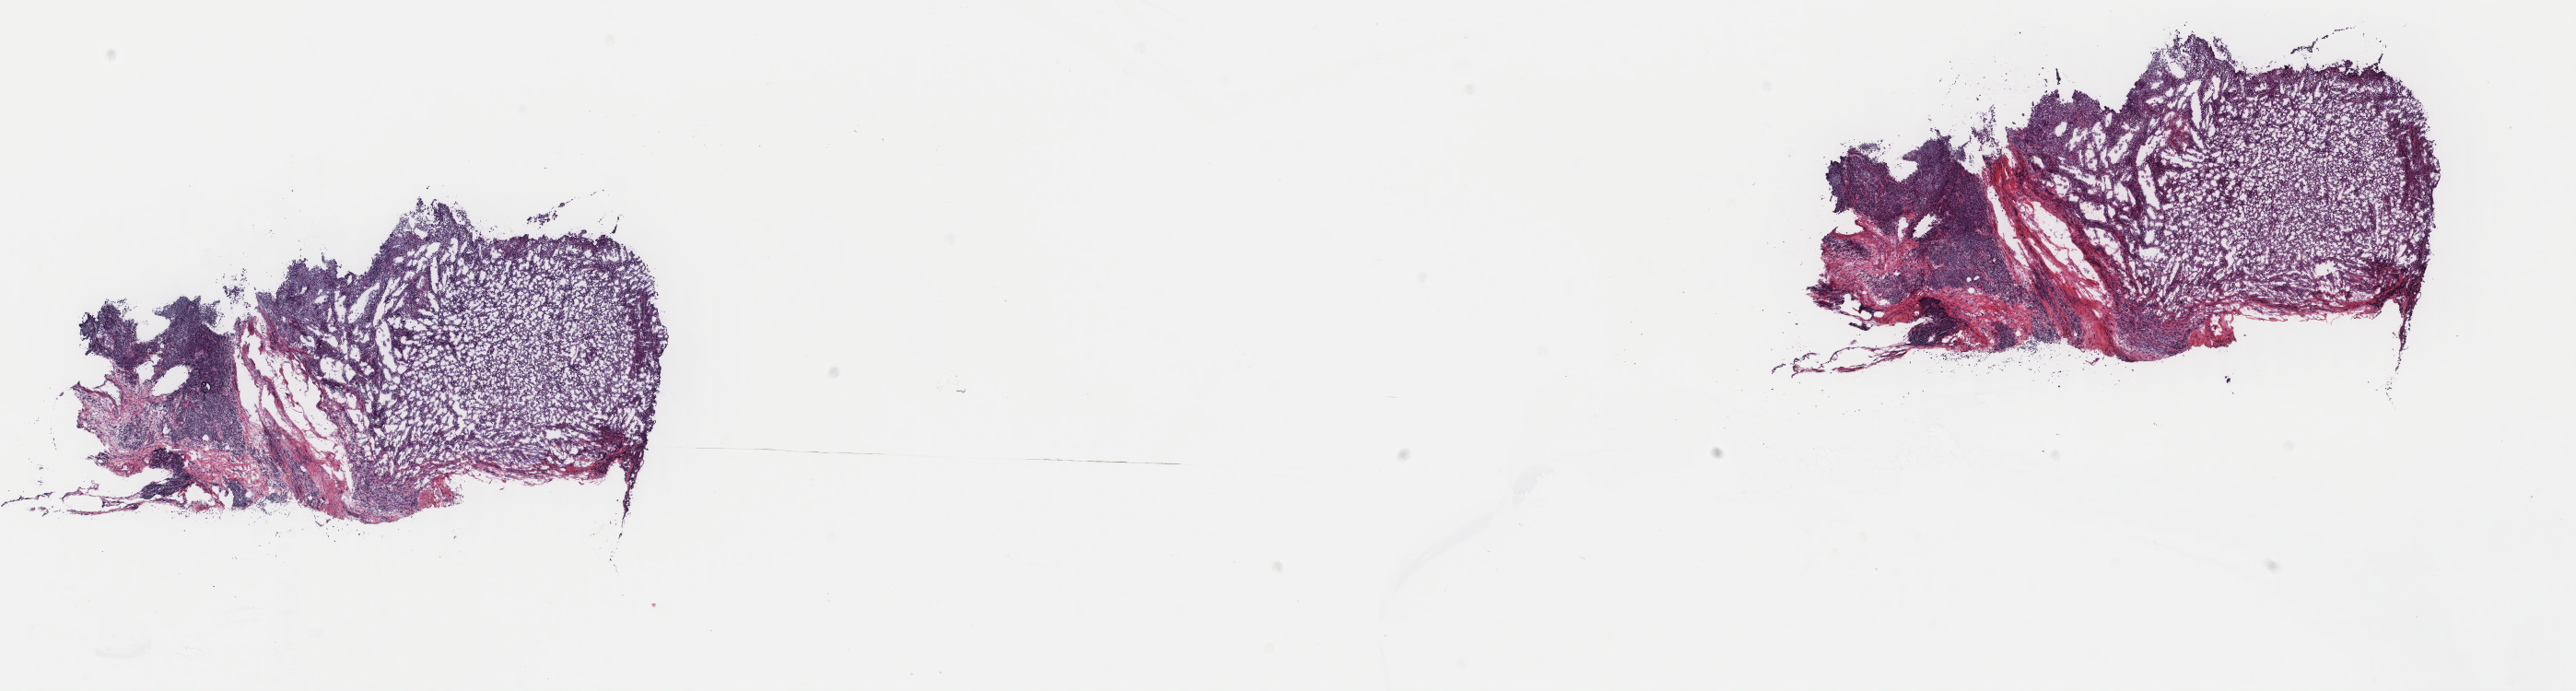
Digitized Hematoxylin and eosin (H&E) stained tissue section (whole slide), shown as a low-resolution overview of the whole scanned area (about 22.2 x 6.0 mm), frozen section from the top of the tissue portion, metastatic tumour sample, sampled site: lymph nodes of axilla or arm. Male, age 51 years at initial diagnosis. Composition of this section per pathologist review: tumour cells 75%, tumour nuclei 80%.
This section: metastatic tumour tissue. Patient diagnosis: Malignant melanoma, NOS.